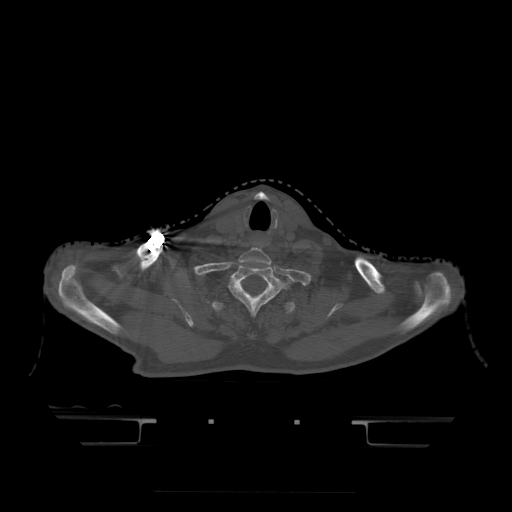
CT including the spine, one axial slice. Position 398 of 522 along the scan axis. Bone window (W 1800 / L 400 HU). 512 × 512 image matrix. Patient age 68 years. Case-level facts recorded for this patient, not image findings: primary cancer: urothelial.
Outlined on this slice (semi-automatic segmentation, software-assisted and operator-edited):
- T1 vertebra: box from (x=229, y=265) to (x=280, y=314) px
- T2 vertebra: (x=212, y=301)–(x=295, y=315)